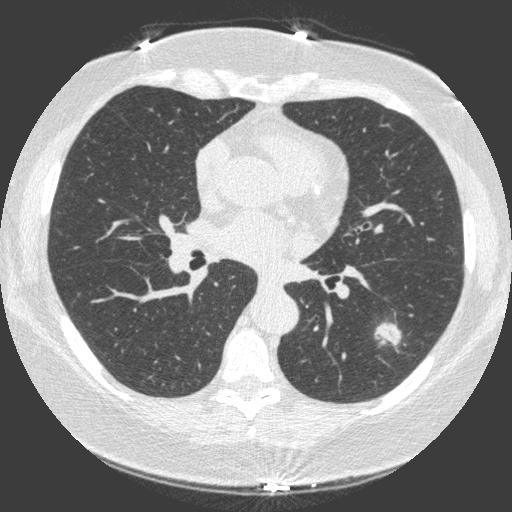
Low-dose screening chest CT, axial slice, third annual screen, lung window (W 1500 / L -600 HU), 1 mm slice thickness, slice 66 of 149 in the series. Female participant, aged 66 years at enrolment.
- Expert reader's lesion annotation, bounding box <362,303,420,356> (left, top, right, bottom; pixels).
- Screening reader's record for this exam (one nodule recorded; not confirmed to be the boxed lesion): non-calcified nodule or mass ≥4 mm, left lower lobe, 23 × 17 mm, spiculated (stellate) margins, soft tissue attenuation, pre-existing on the prior screen: yes; interval growth: yes.
- Official screen result: positive, other.
- Participant outcome: lung cancer diagnosed 15 days after this screen — non-small cell carcinoma, left lower lobe, poorly differentiated (G3), stage IA (AJCC 6th edition), 20 mm at pathology.